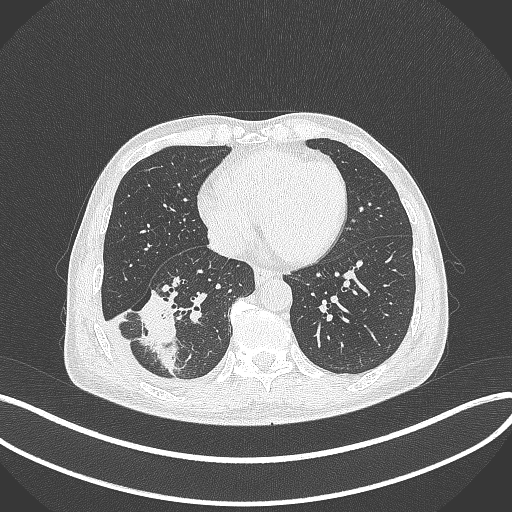
Chest CT, one axial slice; position 133 of 388 along the scan axis; reconstruction kernel B70f; 120 kVp; lung window (W 1500 / L -600 HU); 1 mm slice thickness; 512 × 512 image matrix. Male patient, age 64 years. From the clinical record (not read from this slice): clinical TNM (as recorded): T3 N0 M0; histopathological grade: G2-3.
Annotated regions visible in this slice (bounding box drawn by a radiologist):
- lung tumour (recorded histology: adenocarcinoma): bounding box (x1, y1, x2, y2) in pixels: (129, 280, 183, 379)